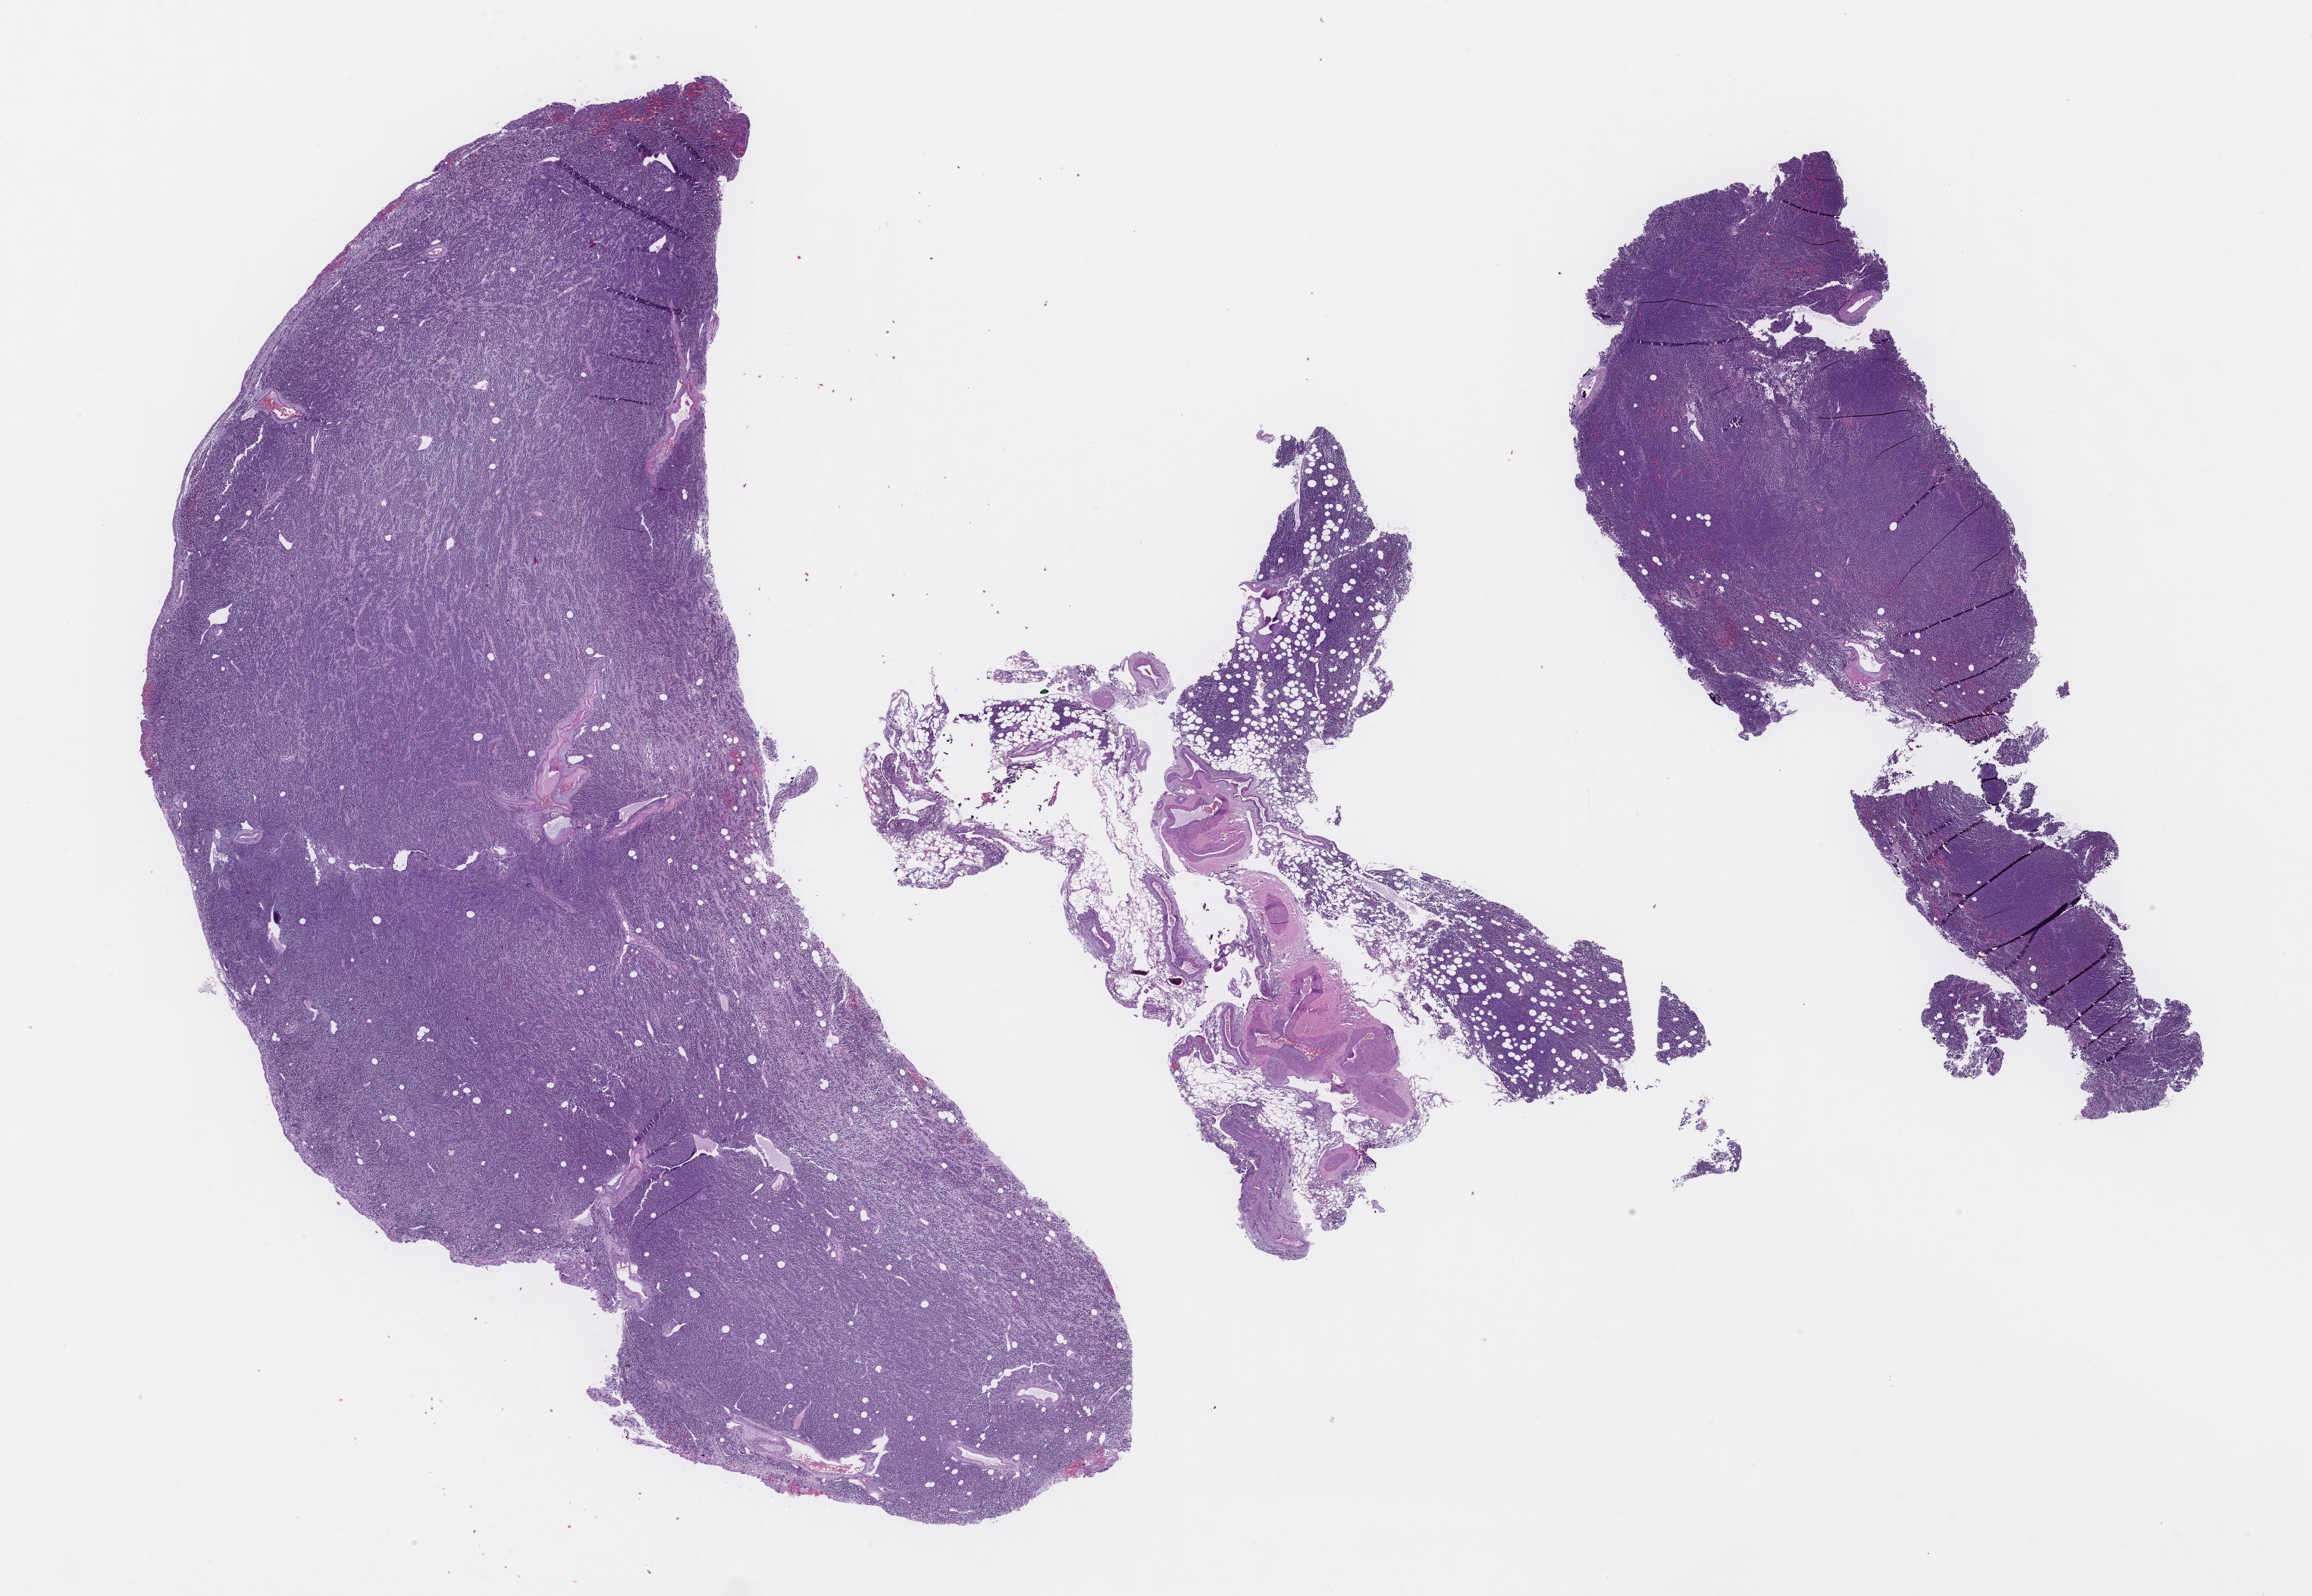
Hematoxylin and eosin (H&E) whole-slide image — whole scanned area (about 24.6 x 17.0 mm) shown as a low-resolution overview. FFPE section. Site: bone marrow. Patient sex: male.
This section: primary tumor. Diagnosis: Plasma Cell Myeloma.